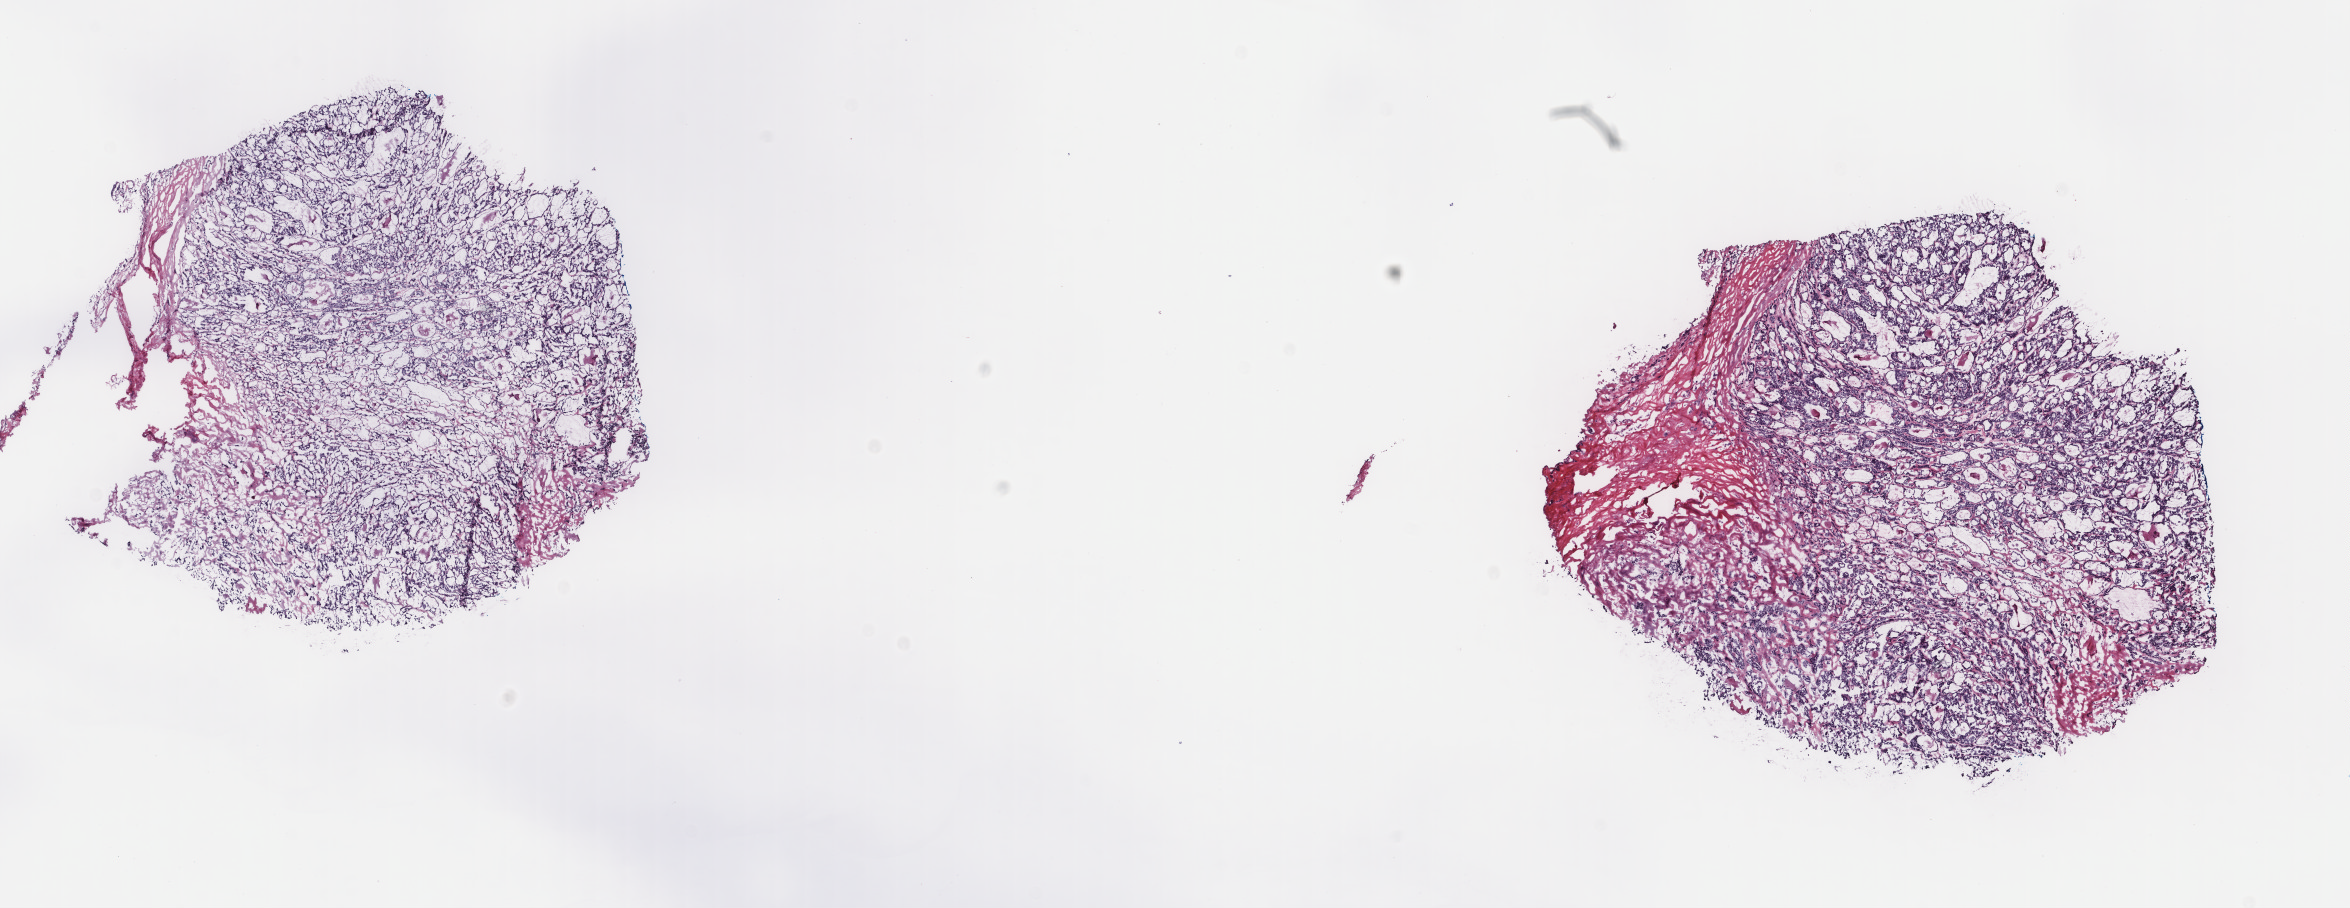
Whole-slide histology image, Hematoxylin and eosin (H&E) stained — whole scanned area (about 18.7 x 7.2 mm, slide scanned at 40x) shown as a low-resolution overview; frozen section from the top of the tissue portion; primary tumour sample from the thyroid. Female patient; age at initial diagnosis 66 years. Composition of this section per pathologist review: tumour cells 80%, tumour nuclei 100%, normal cells 0%, stromal cells 20%, necrosis 0%. Infiltration values recorded for this section: lymphocyte infiltration 0%, monocyte infiltration 2%, neutrophil infiltration 0%.
Lymph nodes positive (case pathology): 0 of 1 examined. AJCC pathologic stage: II (7th edition). Laterality: left. Pathologic diagnosis: Papillary carcinoma, follicular variant (thyroid gland).